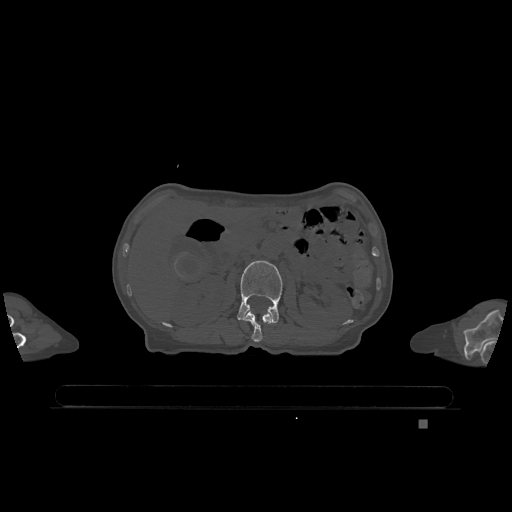
CT including the spine, one axial slice. Position 437 of 1317 along the scan axis. Bone window (W 1800 / L 400 HU). 0.5 mm slice thickness. 512 × 512 image matrix. Patient: female, 74 years. Case-level facts recorded for this patient, not image findings: primary cancer: lung.
Structures marked on this image (semi-automatic segmentation, software-assisted and operator-edited):
- L1 vertebra: bounding box [x1, y1, x2, y2] px = [244, 310, 272, 342]
- L2 vertebra: [237, 260, 283, 323]